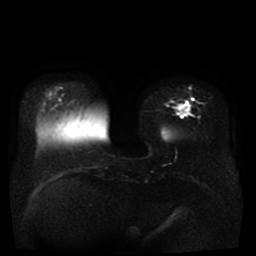
Breast MRI, one axial slice; position 9 of 41 along the scan axis; diffusion-weighted series; image 2 of 4 stored at this slice position (different b-values; order by instance number); 1.5 T; 5 mm slice thickness; 256 × 256 image matrix, field of view 330 × 330 mm. Female patient.
Annotated regions visible in this slice (manually delineated by an expert):
- tumour on diffusion-weighted imaging: bounding box <177,102,189,116> (left, top, right, bottom; pixels)